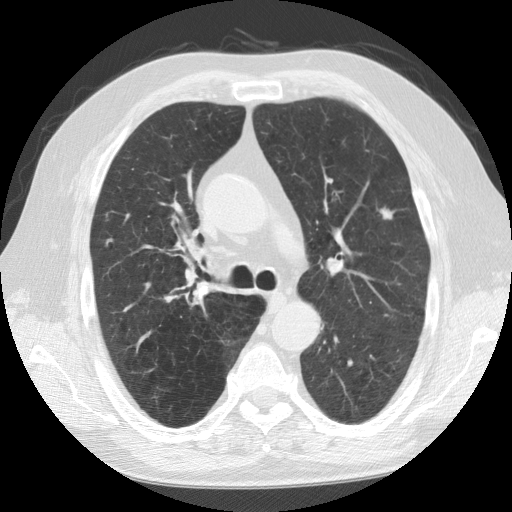
Low-dose screening chest CT, one axial slice; position 67 of 109 along the scan axis; lung window (W 1500 / L -600 HU); 512 × 512 image matrix.
Annotated regions visible in this slice (expert manual segmentation):
- lesion 1 (tumor, upper lobe of left lung): box from (x=379, y=207) to (x=394, y=220) px